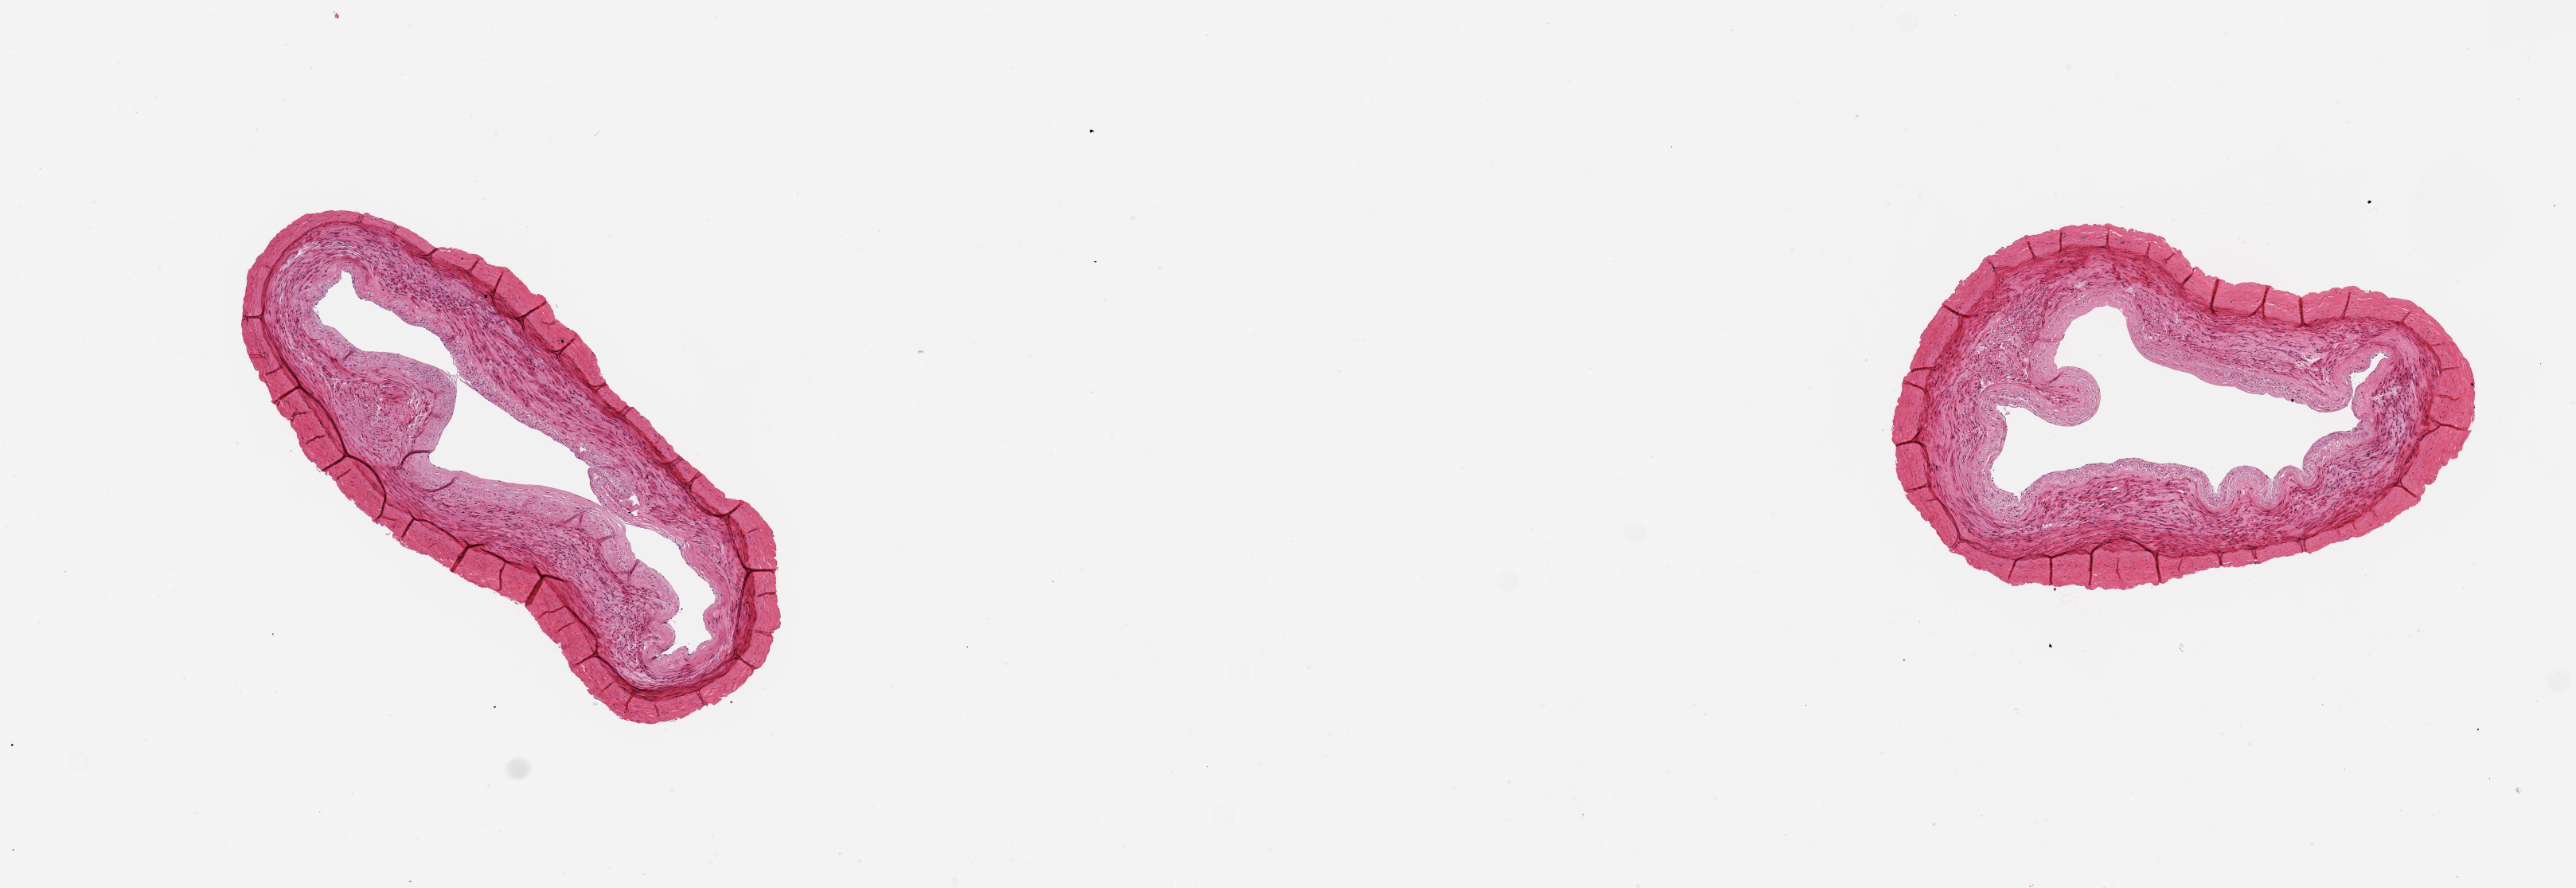
Whole-slide image, hematoxylin and eosin (H&E) stain, brightfield — whole scanned area (about 12.8 x 4.4 mm) shown as a low-resolution overview, PAXgene-fixed paraffin-embedded (PFPE) section, sampled site (target tissue): tibial artery, donor tissue sample. Donor: female.
• review note (as recorded): 2 pieces ~2.5mm d. Excellent clean specimens